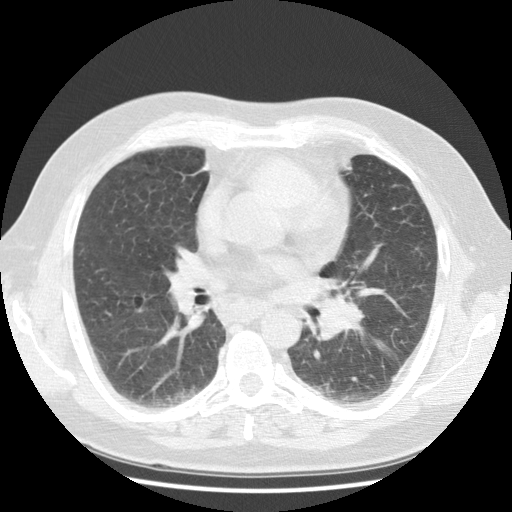
Low-dose screening chest CT, one axial slice; slice 61 of 108 in the series (ordered by position); 120 kVp; lung window (W 1500 / L -600 HU); 2.5 mm slice thickness; 512 × 512 image matrix, field of view 350 × 350 mm.
Annotated regions visible in this slice (outlined manually by an expert reader):
- lesion 1 (tumor, hilum of left lung): bounding box <318,297,363,340> (left, top, right, bottom; pixels)